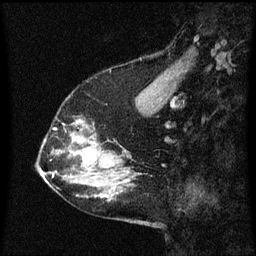
Breast MRI (dynamic contrast-enhanced), one sagittal slice; slice 22 of 60 in the series (ordered by position); dynamic contrast-enhanced series, image 2 of 3 at this slice position (ordered by acquisition); 1.5 T; TE 4.2 ms, TR 8.4 ms; 2 mm slice thickness; 256 × 256 image matrix, field of view 200 × 200 mm. Patient: female, 58 years.
Outlined on this slice (semi-automatically segmented with operator editing):
- analysis volume of interest (the breast-tissue region the enhancement analysis was run in; not a lesion): box from (x=58, y=134) to (x=99, y=151) px
- tumour enhancement mask (voxels above the 70 % enhancement threshold inside the analysis volume of interest): (x=74, y=138)–(x=87, y=151)